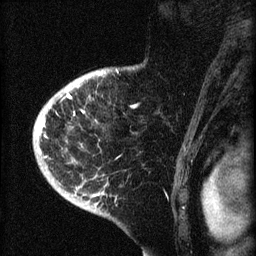
Breast MRI (dynamic contrast-enhanced), one sagittal slice. Position 52 of 60 along the scan axis. Dynamic contrast-enhanced series, image 2 of 4 at this slice position (ordered by acquisition). 1.5 T. TE 4.2 ms, TR 8.2 ms. 2 mm slice thickness. 256 × 256 image matrix. Female patient, age 71 years.
Annotated regions visible in this slice (semi-automatically segmented with operator editing):
- analysis volume of interest (the breast-tissue region the enhancement analysis was run in; not a lesion): bounding box [x1, y1, x2, y2] px = [35, 75, 129, 190]
- tumour enhancement mask (voxels above the 70 % enhancement threshold inside the analysis volume of interest): [35, 90, 85, 158]